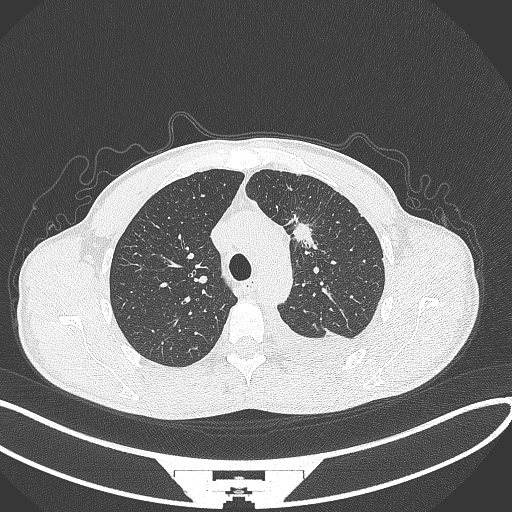
Chest CT, one axial slice. Slice 247 of 371 in the series (ordered by position). 120 kVp. Lung window (W 1500 / L -600 HU). 1 mm slice thickness. 512 × 512 image matrix, field of view 400 × 400 mm. Male patient, age 49 years. Case-level facts recorded for this patient, not image findings: clinical TNM (as recorded): T1c N1 M1.
Structures marked on this image (rectangle marked by the reading radiologist):
- lung tumour (recorded histology: adenocarcinoma): bounding box [x1, y1, x2, y2] px = [285, 211, 315, 249]